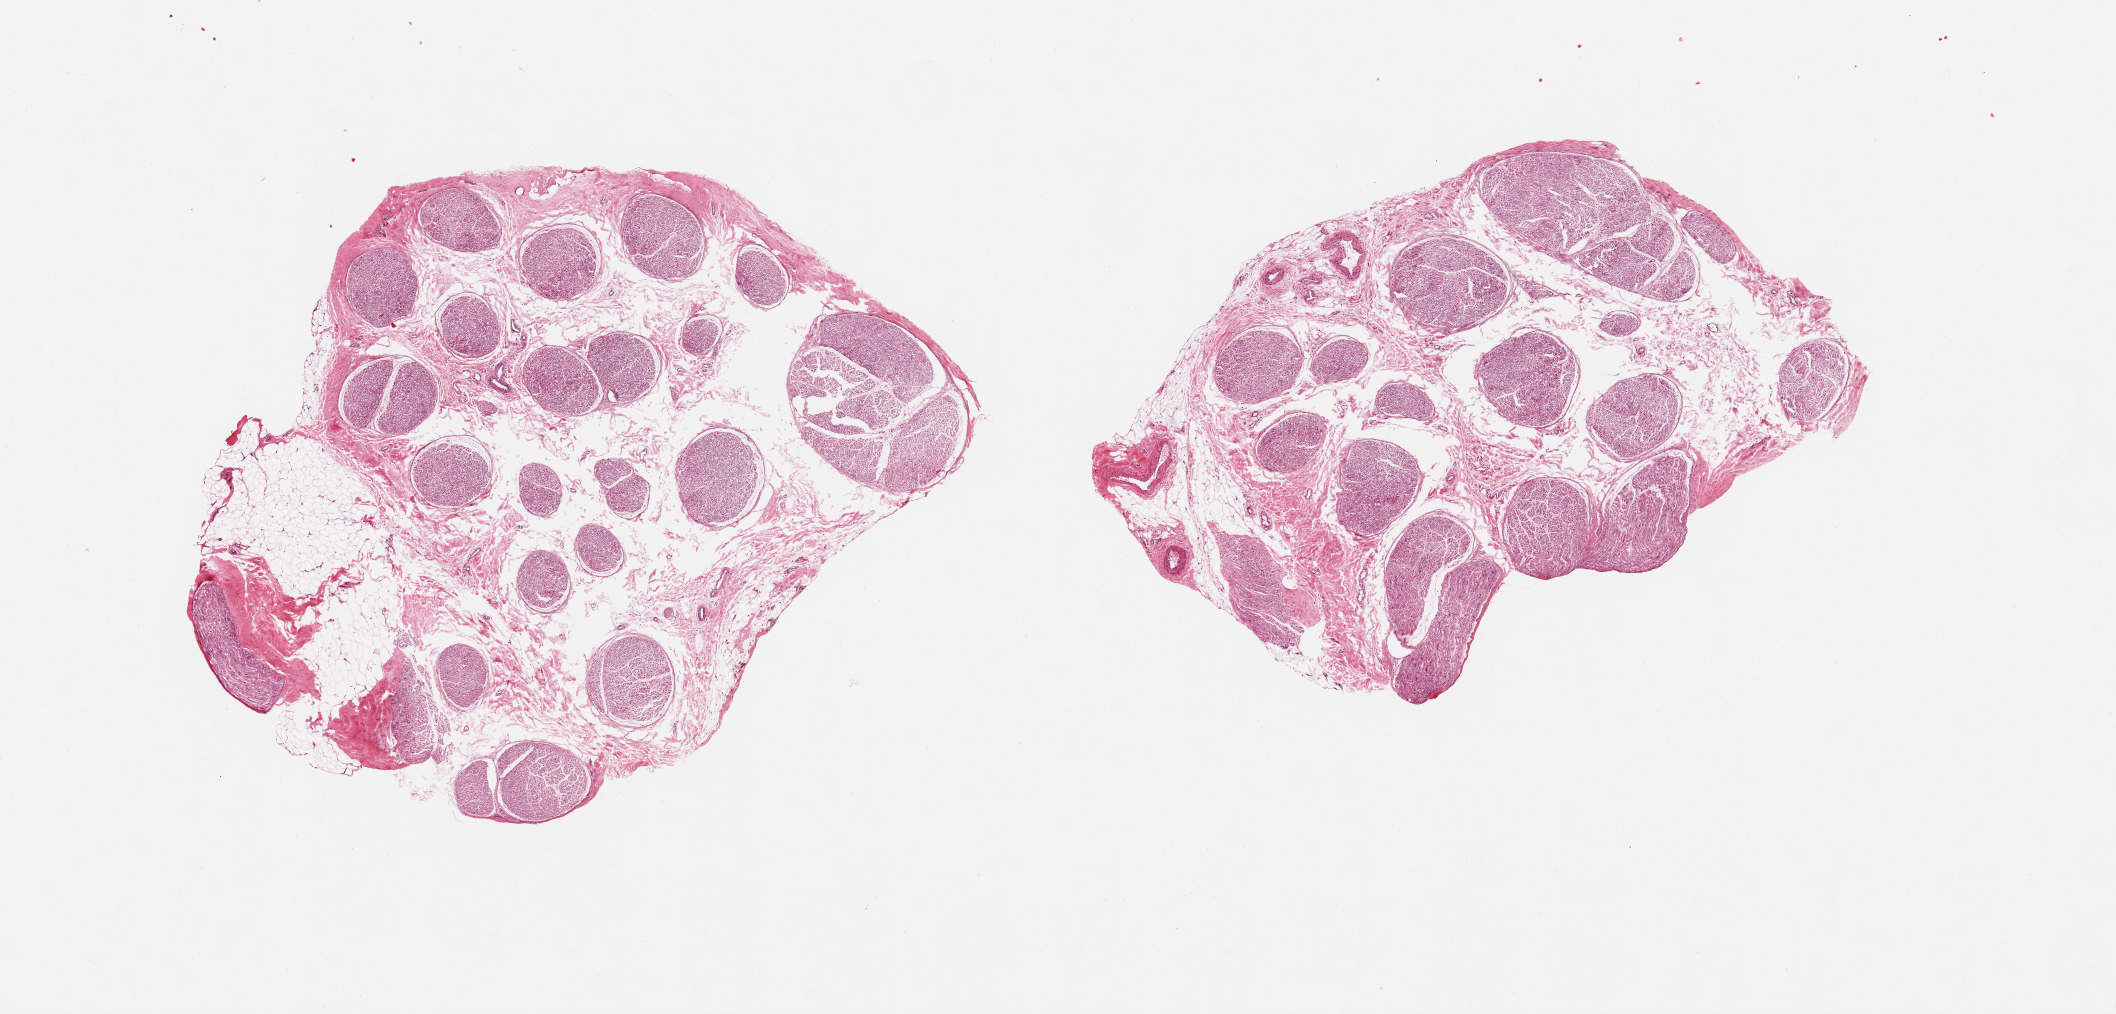
Digitized H&E-stained section, brightfield, a low-resolution overview of the entire scanned area, about 16.7 x 8.0 mm (slide scanned at 20x). PAXgene-fixed, paraffin-embedded tissue. Target tissue: tibial nerve. Tissue donor sample. Donor sex: female.
Reviewer comment on this tissue sample: 2 aliquots, ~ 4.5mm d. Good clean specimens.